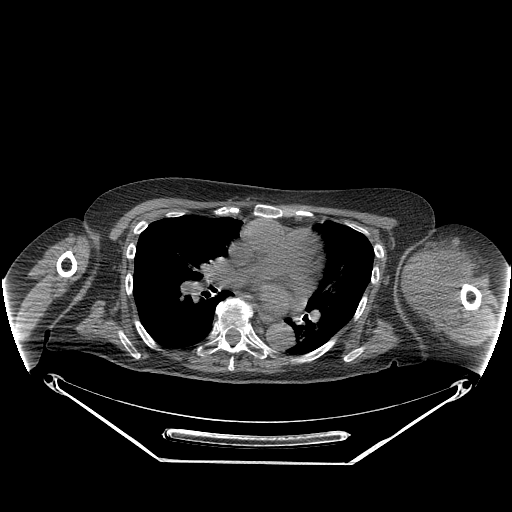
CT of an extremity soft-tissue mass (from a PET/CT study), one axial slice; position 176 of 267 along the scan axis; reconstruction kernel STANDARD; 140 kVp; soft-tissue window (W 400 / L 40 HU); 512 × 512 image matrix. Female patient. From the clinical record (not read from this slice): histological type: pleiomorphic leiomyosarcoma; grade: high; site of the primary tumour: left biceps.
Structures marked on this image (expert contour drawn on MRI and transferred to this co-registered scan by the dataset authors):
- gross tumour volume including surrounding oedema: bounding box <406,237,469,325> (left, top, right, bottom; pixels)
- gross tumour volume (mass): <406,238,465,311>